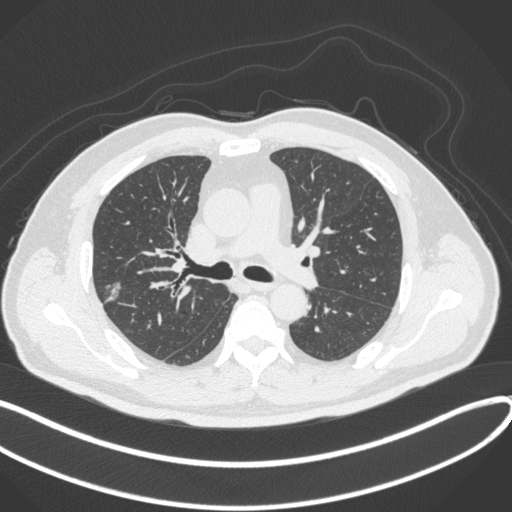
Chest CT, one axial slice. Slice 212 of 373 in the series (ordered by position). Reconstruction kernel B31f. Lung window (W 1500 / L -600 HU). 1 mm slice thickness. 512 × 512 image matrix, field of view 400 × 400 mm. Patient: male, 60 years. From the clinical record (not read from this slice): clinical TNM (as recorded): T1c N0 M0.
Outlined on this slice (rectangle marked by the reading radiologist):
- lung tumour (recorded histology: adenocarcinoma): box from (x=99, y=279) to (x=127, y=313) px